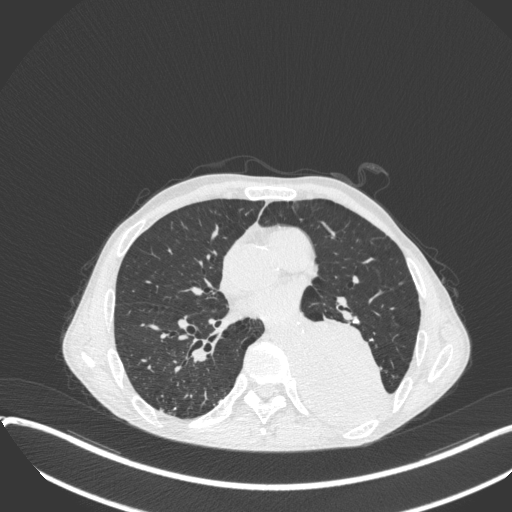
Chest CT, one axial slice; slice 173 of 400 in the series (ordered by position); lung window (W 1500 / L -600 HU); 1 mm slice thickness; 512 × 512 image matrix. Patient: male, 57 years. Case-level facts recorded for this patient, not image findings: clinical TNM (as recorded): T4 N0 M0.
Annotated regions visible in this slice (rectangle marked by the reading radiologist):
- lung tumour (recorded histology: squamous cell carcinoma): bounding box (x1, y1, x2, y2) in pixels: (296, 312, 394, 428)